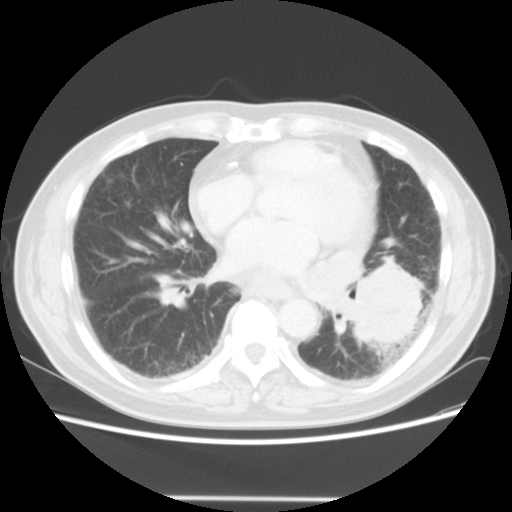
Chest CT, one axial slice. Slice 20 of 56 in the series (ordered by position). Reconstruction kernel STANDARD. 140 kVp. Lung window (W 1500 / L -600 HU). 5 mm slice thickness. 512 × 512 image matrix, field of view 360 × 360 mm. Male patient, age 66 years. Case-level facts recorded for this patient, not image findings: clinical TNM (as recorded): T4 N3 M0; histopathological grade: G3.
Annotated regions visible in this slice (bounding box drawn by a radiologist):
- lung tumour (recorded histology: small cell carcinoma): bounding box (x1, y1, x2, y2) in pixels: (341, 258, 423, 352)